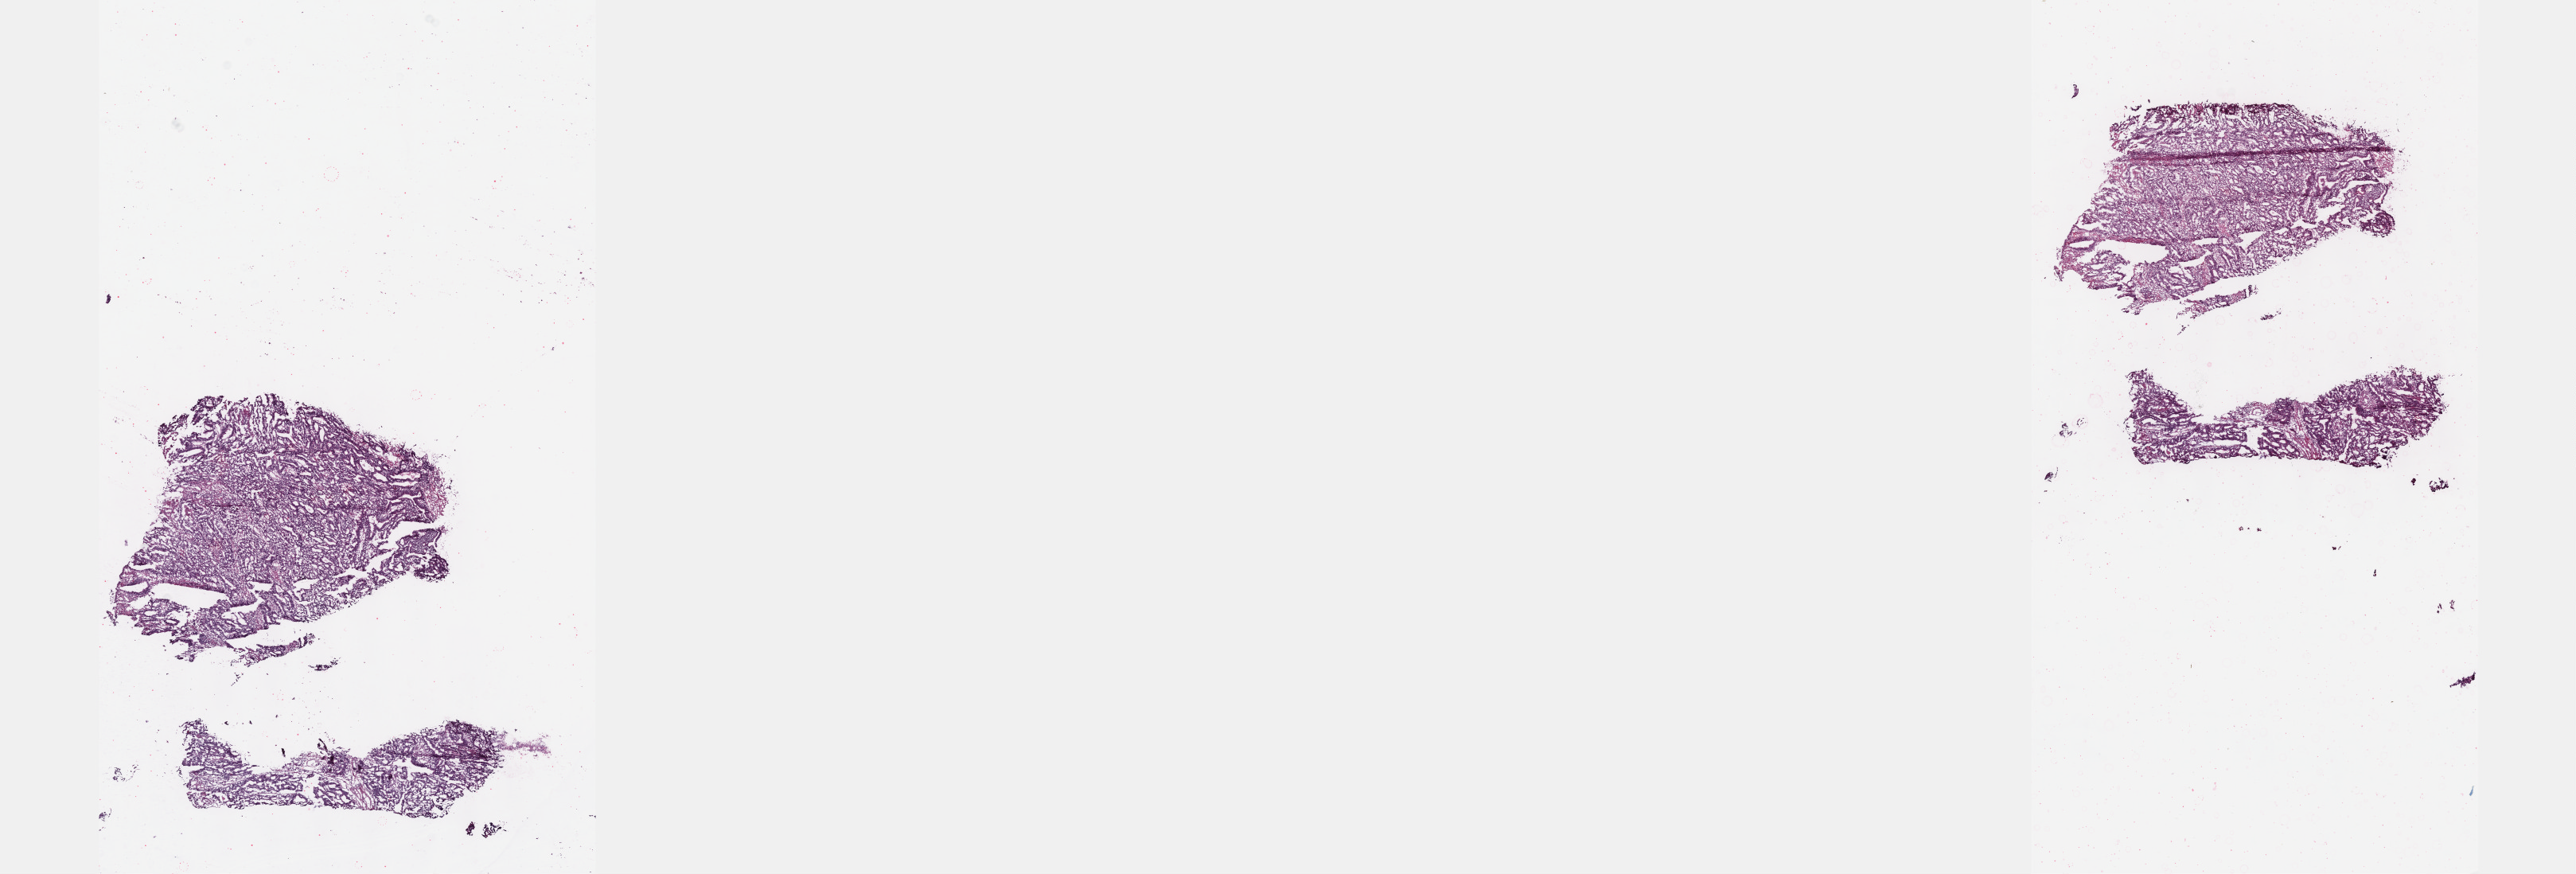
Whole-slide histology image, H&E — shown as a low-resolution overview of the whole scanned area (about 26.2 x 8.9 mm); frozen section; primary tumour sample from the rectum. Male, age 66 years at initial diagnosis. Slide review estimates, as recorded: tumour cells 90%, tumour nuclei 75%, normal cells 0%, stromal cells 8%, necrosis 2%. Inflammatory infiltration, as recorded: lymphocyte infiltration 12%, monocyte infiltration 3%, neutrophil infiltration 2%.
AJCC pathologic stage: IV. Histologic diagnosis: Adenocarcinoma, NOS.